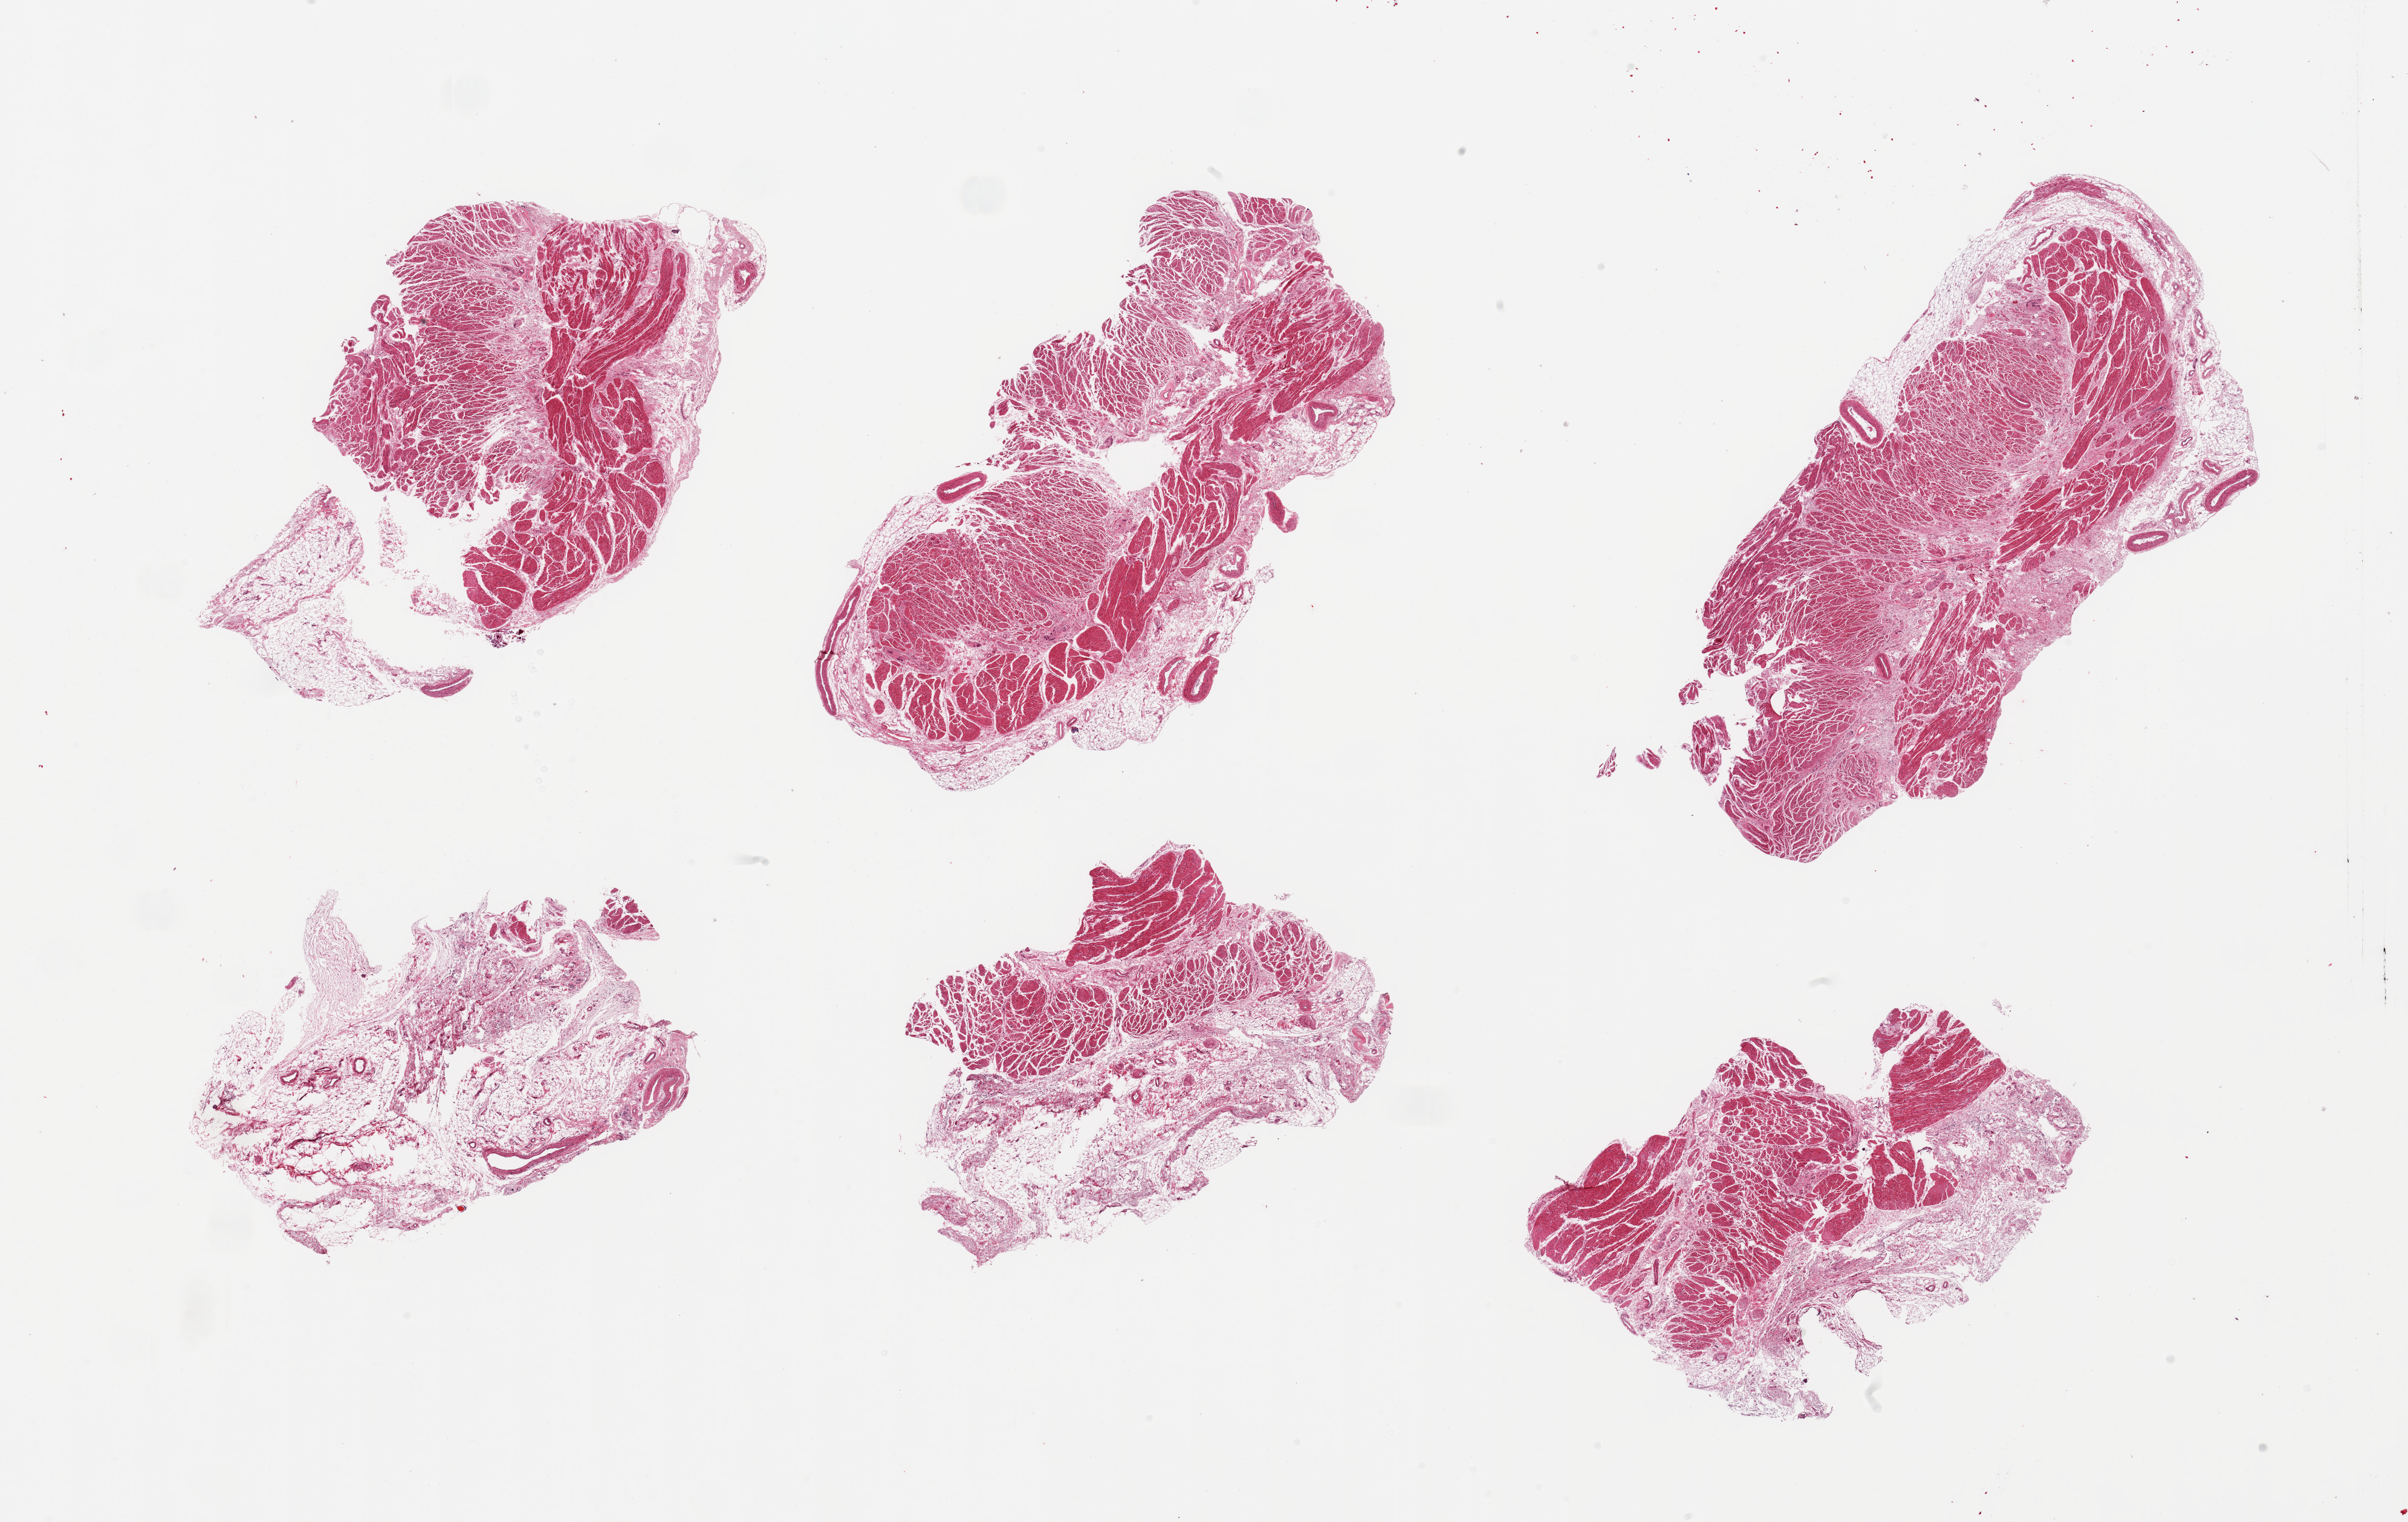
Whole-slide image, haematoxylin and eosin stain — low-resolution overview of the scanned area, about 31.5 x 19.9 mm, PAXgene-fixed paraffin-embedded (PFPE) section, section of esophageal muscle (target tissue), donor tissue sample. Male donor.
• review note (as recorded): 6 pieces; confirmed target muscularis propria, however, one piece contains only small fragment; fibrofatty tissue (all pieces), up to ~2mm, focal collections of inflammatory cells